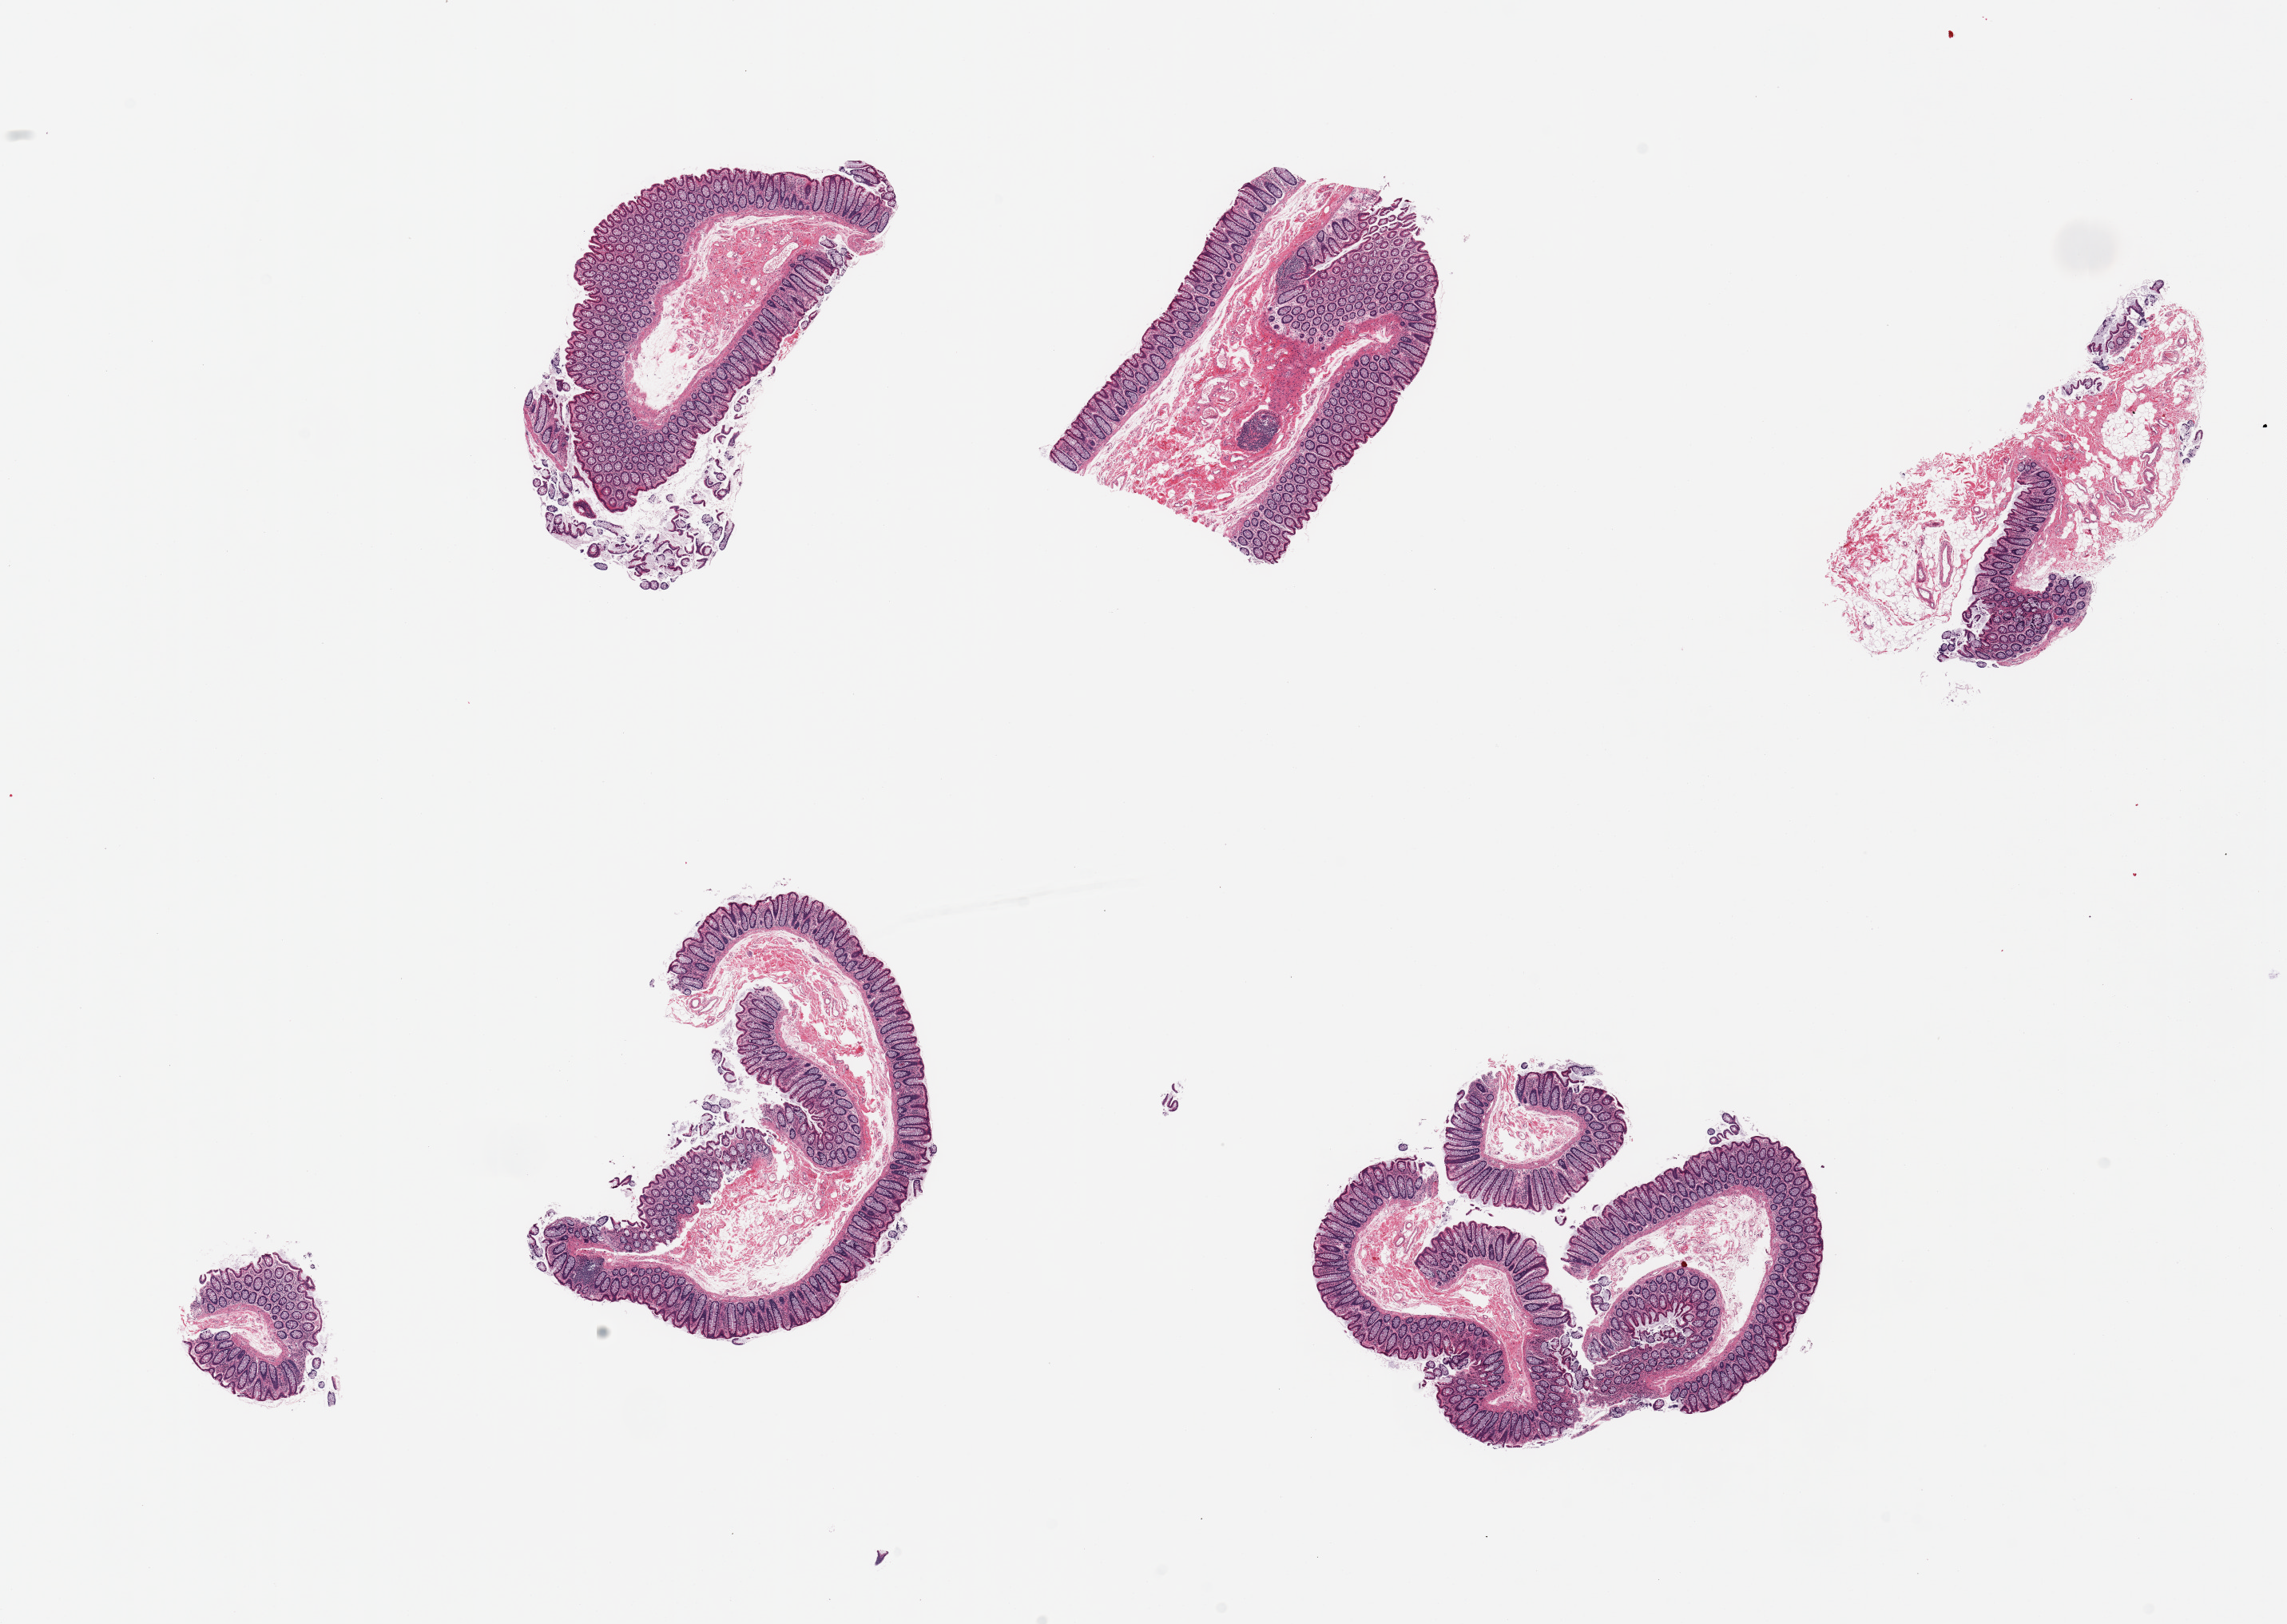
H&E whole-slide image, brightfield — whole scanned area (about 22.6 x 16.1 mm, acquisition: 20x scan) shown as a low-resolution overview; PAXgene-fixed paraffin-embedded (PFPE) section; target tissue: transverse colon; donor tissue sample.
Pathologist's review note for this sample: 6 pieces, well presreved mucosa up to ~0.5mm thick.